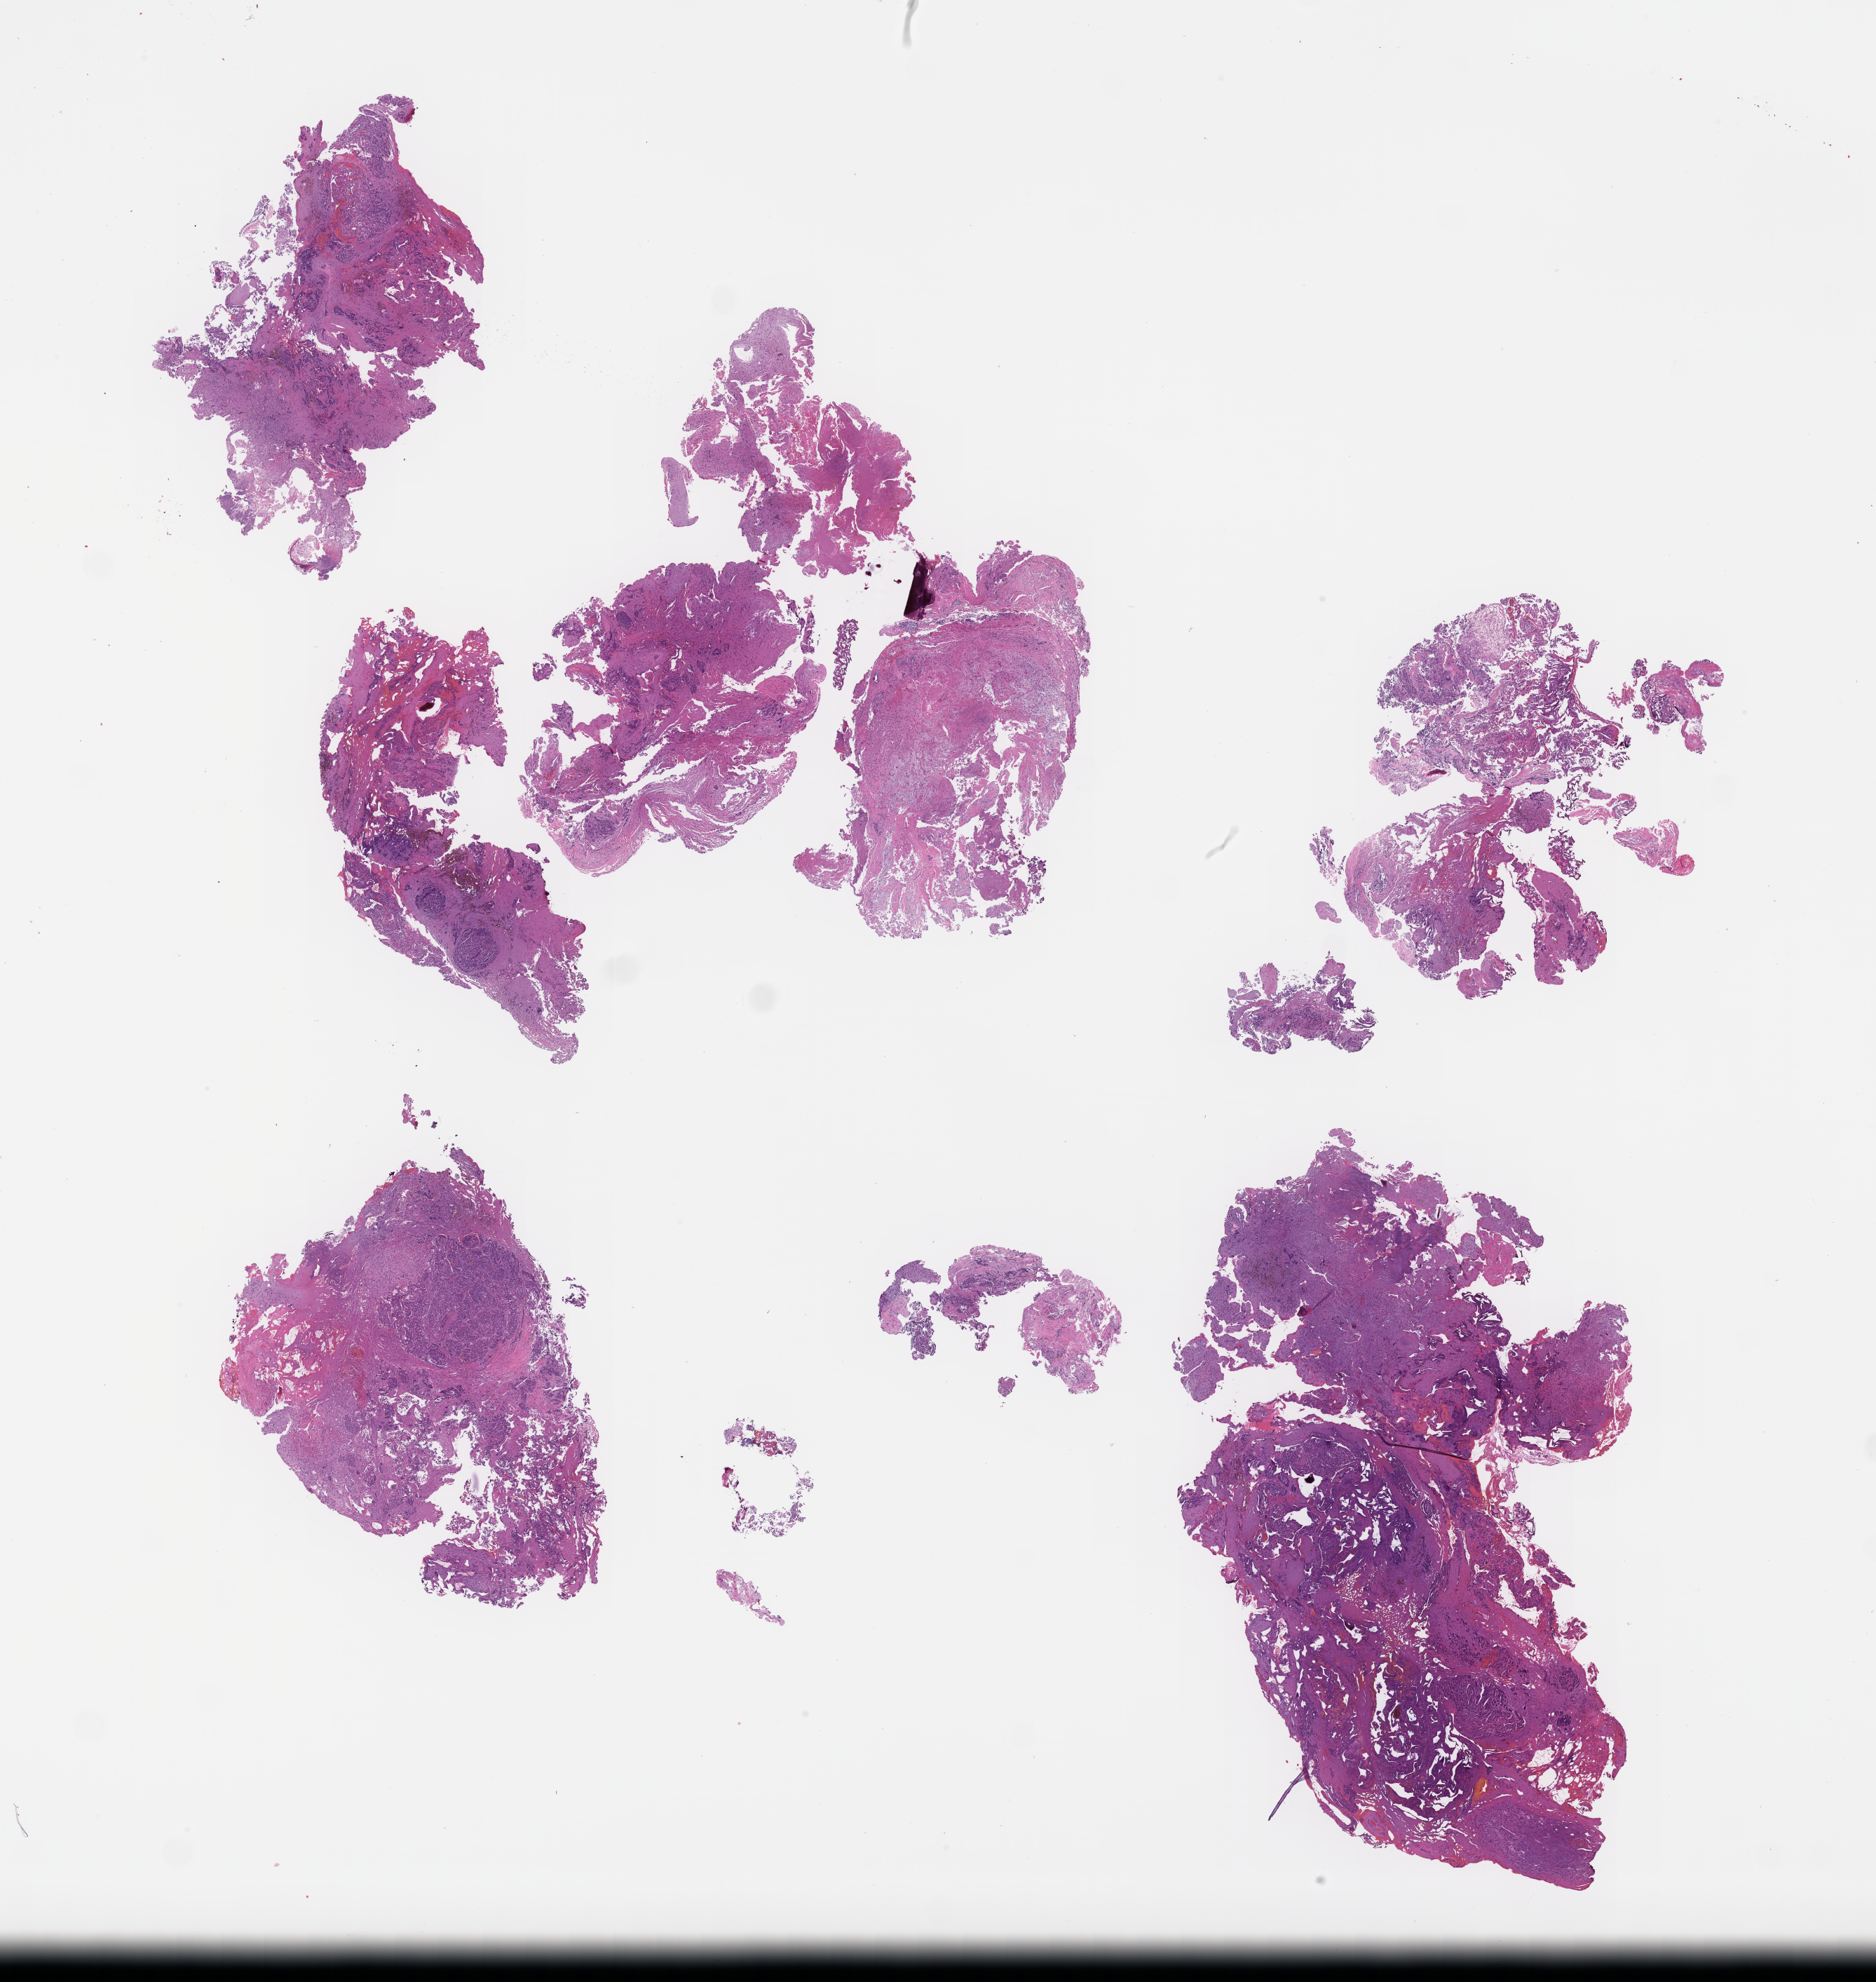
H&E whole-slide image — shown as a low-resolution overview of the whole scanned area (about 21.6 x 22.8 mm); FFPE section; archival tissue. Patient: female.
This section: metastasis (sampled organ not recorded). Patient diagnosis (primary): Invasive Breast Carcinoma.